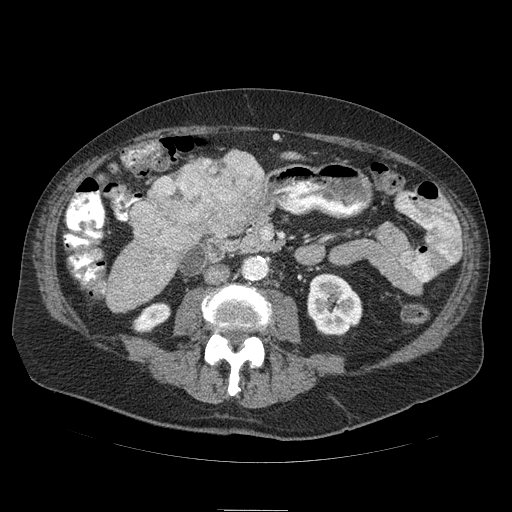
Contrast-enhanced abdominal CT (liver protocol), one axial slice; slice 19 of 103 in the series (ordered by position); reconstruction kernel STANDARD; 120 kVp; soft-tissue window (W 400 / L 40 HU); 512 × 512 image matrix. From the clinical record (not read from this slice): diagnosis: hepatocellular carcinoma (patient treated with transarterial chemoembolisation; whether this scan precedes or follows treatment is not stated here); TNM stage (as recorded): Stage-IIIA; Child-Pugh class: B; tumour differentiation: well differentiated; tumour nodularity: multinodular.
Outlined on this slice (semi-automatic segmentation, software-assisted and operator-edited):
- liver parenchyma outside the tumour (the mass and vessels are separate outlines, so this box may not span the whole liver): bounding box (x1, y1, x2, y2) in pixels: (217, 150, 268, 226)
- mass: (131, 151, 269, 265)